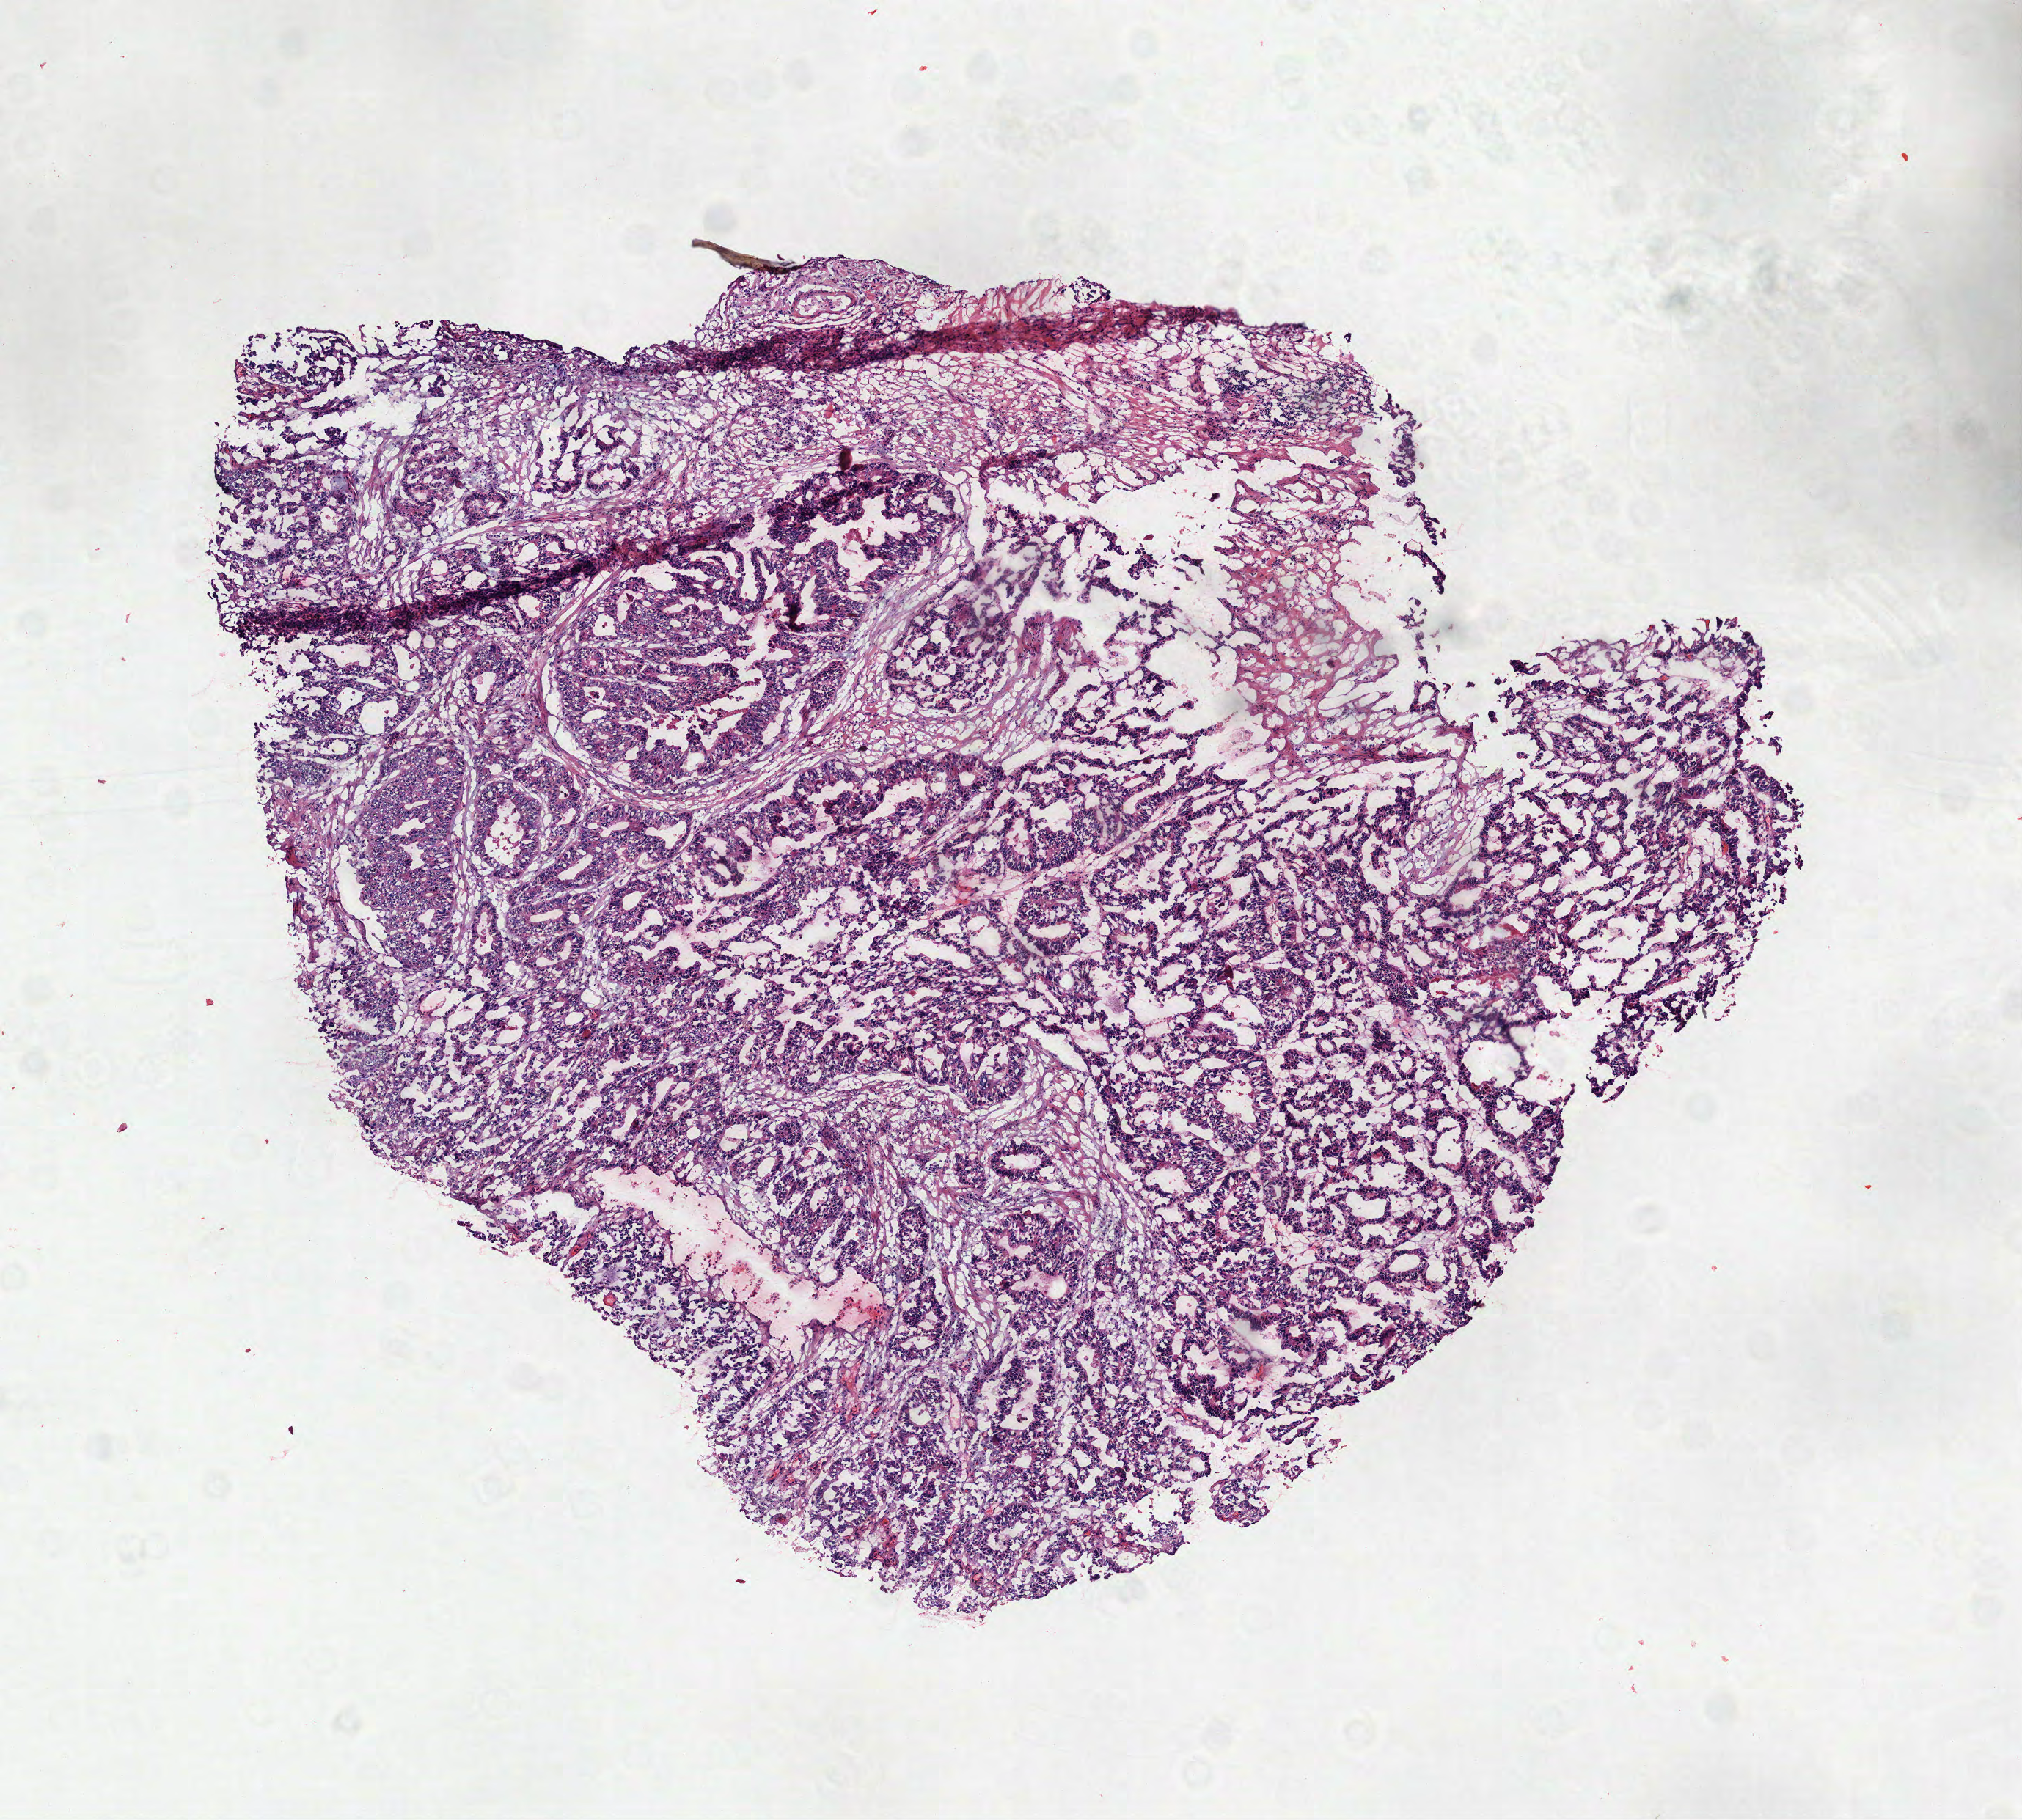
Hematoxylin and eosin (H&E) stained whole-slide image, shown as a low-resolution overview of the whole scanned area (about 5.6 x 5.0 mm, slide scanned at 40x), frozen section from the top of the tissue portion, colon, primary tumour sample. Patient: male, age at initial diagnosis 81 years. Pathologist review of this section (percent, as recorded): tumour cells 85%, tumour nuclei 80%, normal cells 0%, stromal cells 15%, necrosis 0%.
AJCC pathologic stage: I. Pathologic diagnosis: Adenocarcinoma, NOS (ascending colon).